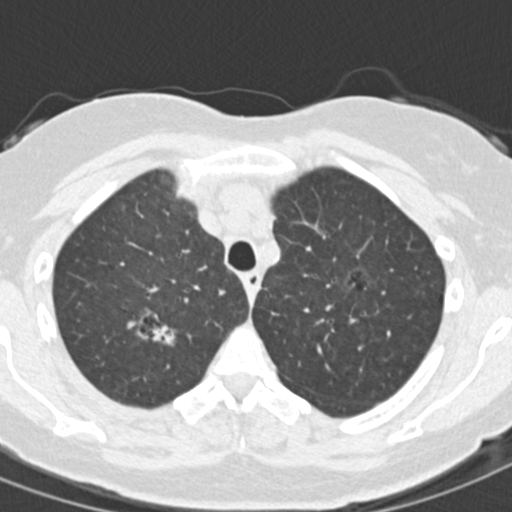
Low-dose screening chest CT, one axial slice; slice 121 of 157 in the series (ordered by position); lung window (W 1500 / L -600 HU); 2 mm slice thickness; 512 × 512 image matrix, field of view 280 × 280 mm.
Structures marked on this image (expert manual segmentation):
- lesion 1 (tumor, upper lobe of right lung): bounding box [x1, y1, x2, y2] px = [127, 307, 178, 348]